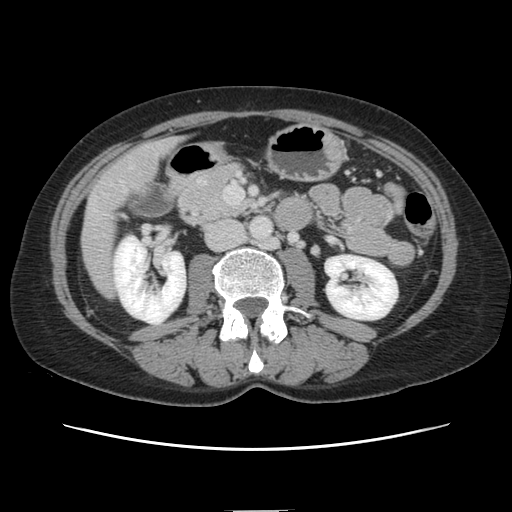
Contrast-enhanced abdominal CT, one axial slice; position 41 of 141 along the scan axis; 120 kVp; intravenous contrast given; soft-tissue window (W 400 / L 40 HU); 2.5 mm slice thickness; 512 × 512 image matrix. Female patient, age 63 years. From the clinical record (not read from this slice): diagnosis: colorectal cancer liver metastases, imaged before liver resection; multiple liver metastases: yes; largest metastasis: 3.2 cm; chemotherapy before resection: yes.
Structures marked on this image (manually delineated by an expert):
- liver: bounding box <82,139,178,294> (left, top, right, bottom; pixels)